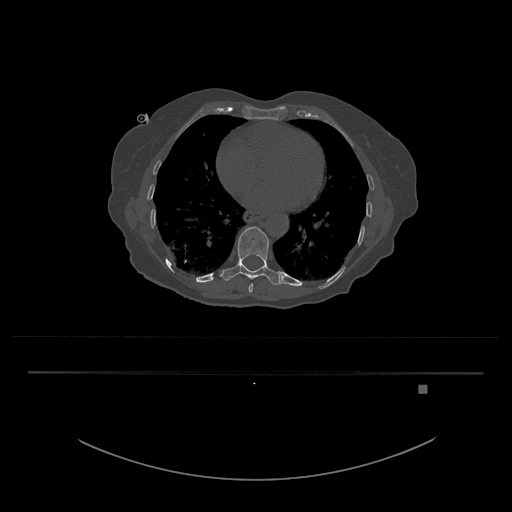
CT including the spine, one axial slice. Position 720 of 797 along the scan axis. Reconstruction kernel Br40s/3. Bone window (W 1800 / L 400 HU). 512 × 512 image matrix, field of view 500 × 500 mm. Patient: female, 57 years. From the clinical record (not read from this slice): primary cancer: cervical.
Structures marked on this image (semi-automatically segmented with operator editing):
- T10 vertebra: bounding box (x1, y1, x2, y2) in pixels: (220, 226, 285, 285)
- T9 vertebra: (248, 284, 253, 293)